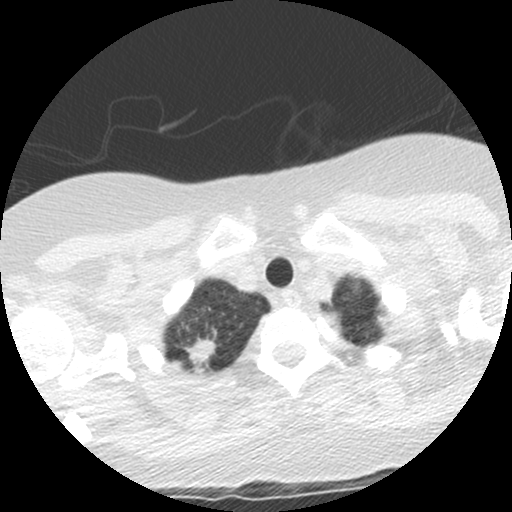
Low-dose screening chest CT, one axial slice; position 120 of 130 along the scan axis; reconstruction kernel STANDARD; lung window (W 1500 / L -600 HU); 2.5 mm slice thickness; 512 × 512 image matrix.
Annotated regions visible in this slice (manually delineated by an expert):
- lesion 1 (tumor, upper lobe of right lung): bounding box [x1, y1, x2, y2] px = [187, 340, 215, 363]